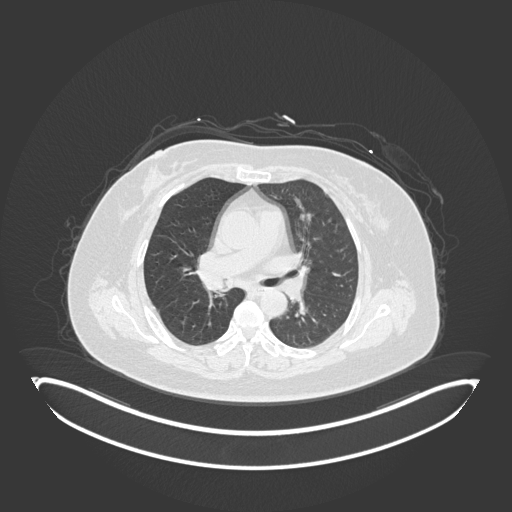
Chest CT, one axial slice; slice 94 of 245 in the series (ordered by position); reconstruction kernel B30f; 120 kVp; lung window (W 1500 / L -600 HU); 1 mm slice thickness; 512 × 512 image matrix, field of view 500 × 500 mm. Female patient, age 60 years. From the clinical record (not read from this slice): clinical TNM (as recorded): T1c N0 M0; histopathological grade: G1-G2.
Annotated regions visible in this slice (rectangle marked by the reading radiologist):
- lung tumour (recorded histology: squamous cell carcinoma): box from (x=202, y=272) to (x=233, y=292) px